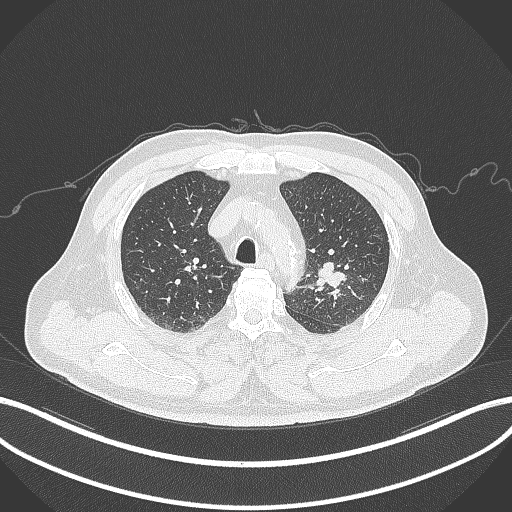
Chest CT, one axial slice. Position 234 of 286 along the scan axis. Lung window (W 1500 / L -600 HU). 512 × 512 image matrix, field of view 400 × 400 mm. Male patient, age 67 years. From the clinical record (not read from this slice): clinical TNM (as recorded): T2a N1 M0.
Outlined on this slice (rectangle marked by the reading radiologist):
- lung tumour (recorded histology: adenocarcinoma): bounding box [x1, y1, x2, y2] px = [314, 258, 349, 290]